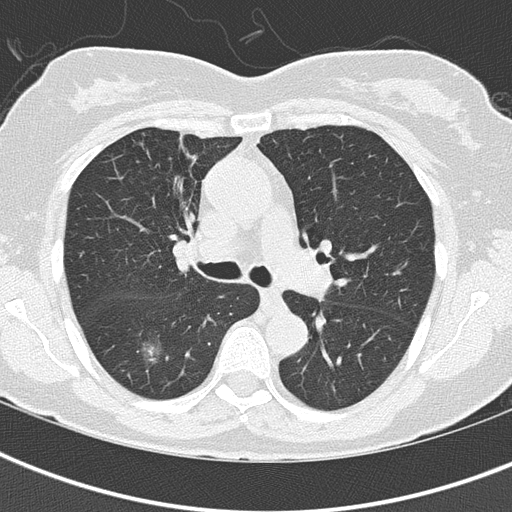
Low-dose screening chest CT, axial slice, first (baseline) screen, lung window (W 1500 / L -600 HU), 2 mm slice thickness, 120 kVp, 512 × 512 image matrix. Female participant, aged 68 years at enrolment.
Expert-annotated lung lesion, bounding box [x1, y1, x2, y2] px = [122, 326, 179, 376]. Screening reader's record for this exam (one nodule recorded; not confirmed to be the boxed lesion): non-calcified nodule or mass ≥4 mm, right lower lobe, 19 × 17 mm, spiculated (stellate) margins, ground glass attenuation. Official screen result: positive, change unspecified: nodule(s) >= 4 mm or enlarging nodule(s), mass(es), or other non-specific abnormalities suspicious for lung cancer.